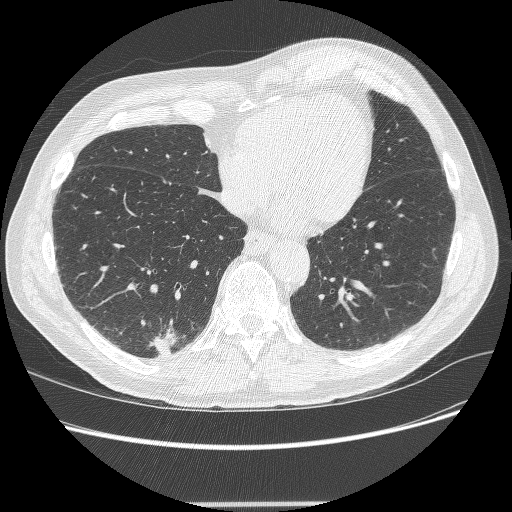
Low-dose screening chest CT, axial slice, second screening round (one year after baseline), lung window (W 1500 / L -600 HU), 1.25 mm slice thickness, slice 75 of 245 in the series, 512 × 512 image matrix, field of view 372 × 372 mm. Male, age 71 years at enrolment. Current smoker at enrolment.
Expert reader's lesion annotation, bounding box <137,323,190,365> (left, top, right, bottom; pixels). The screening reader recorded 5 non-calcified nodules or masses ≥4 mm on this exam; which of them this box marks is not recorded.